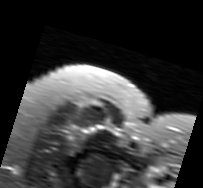
MRI of an extremity soft-tissue mass, one axial slice; T2-weighted fat-saturated; MR volume resampled by the dataset authors to the PET/CT grid (not the native acquisition matrix); 3.27 mm slice thickness; 203 × 188 image matrix. Female patient. Case-level facts recorded for this patient, not image findings: histological type: malignant solitary fibrous tumor; grade: intermediate; site of the primary tumour: right thigh.
Outlined on this slice (expert contour drawn on MRI and transferred to this co-registered scan by the dataset authors):
- gross tumour volume including surrounding oedema: bounding box [x1, y1, x2, y2] px = [67, 122, 114, 148]